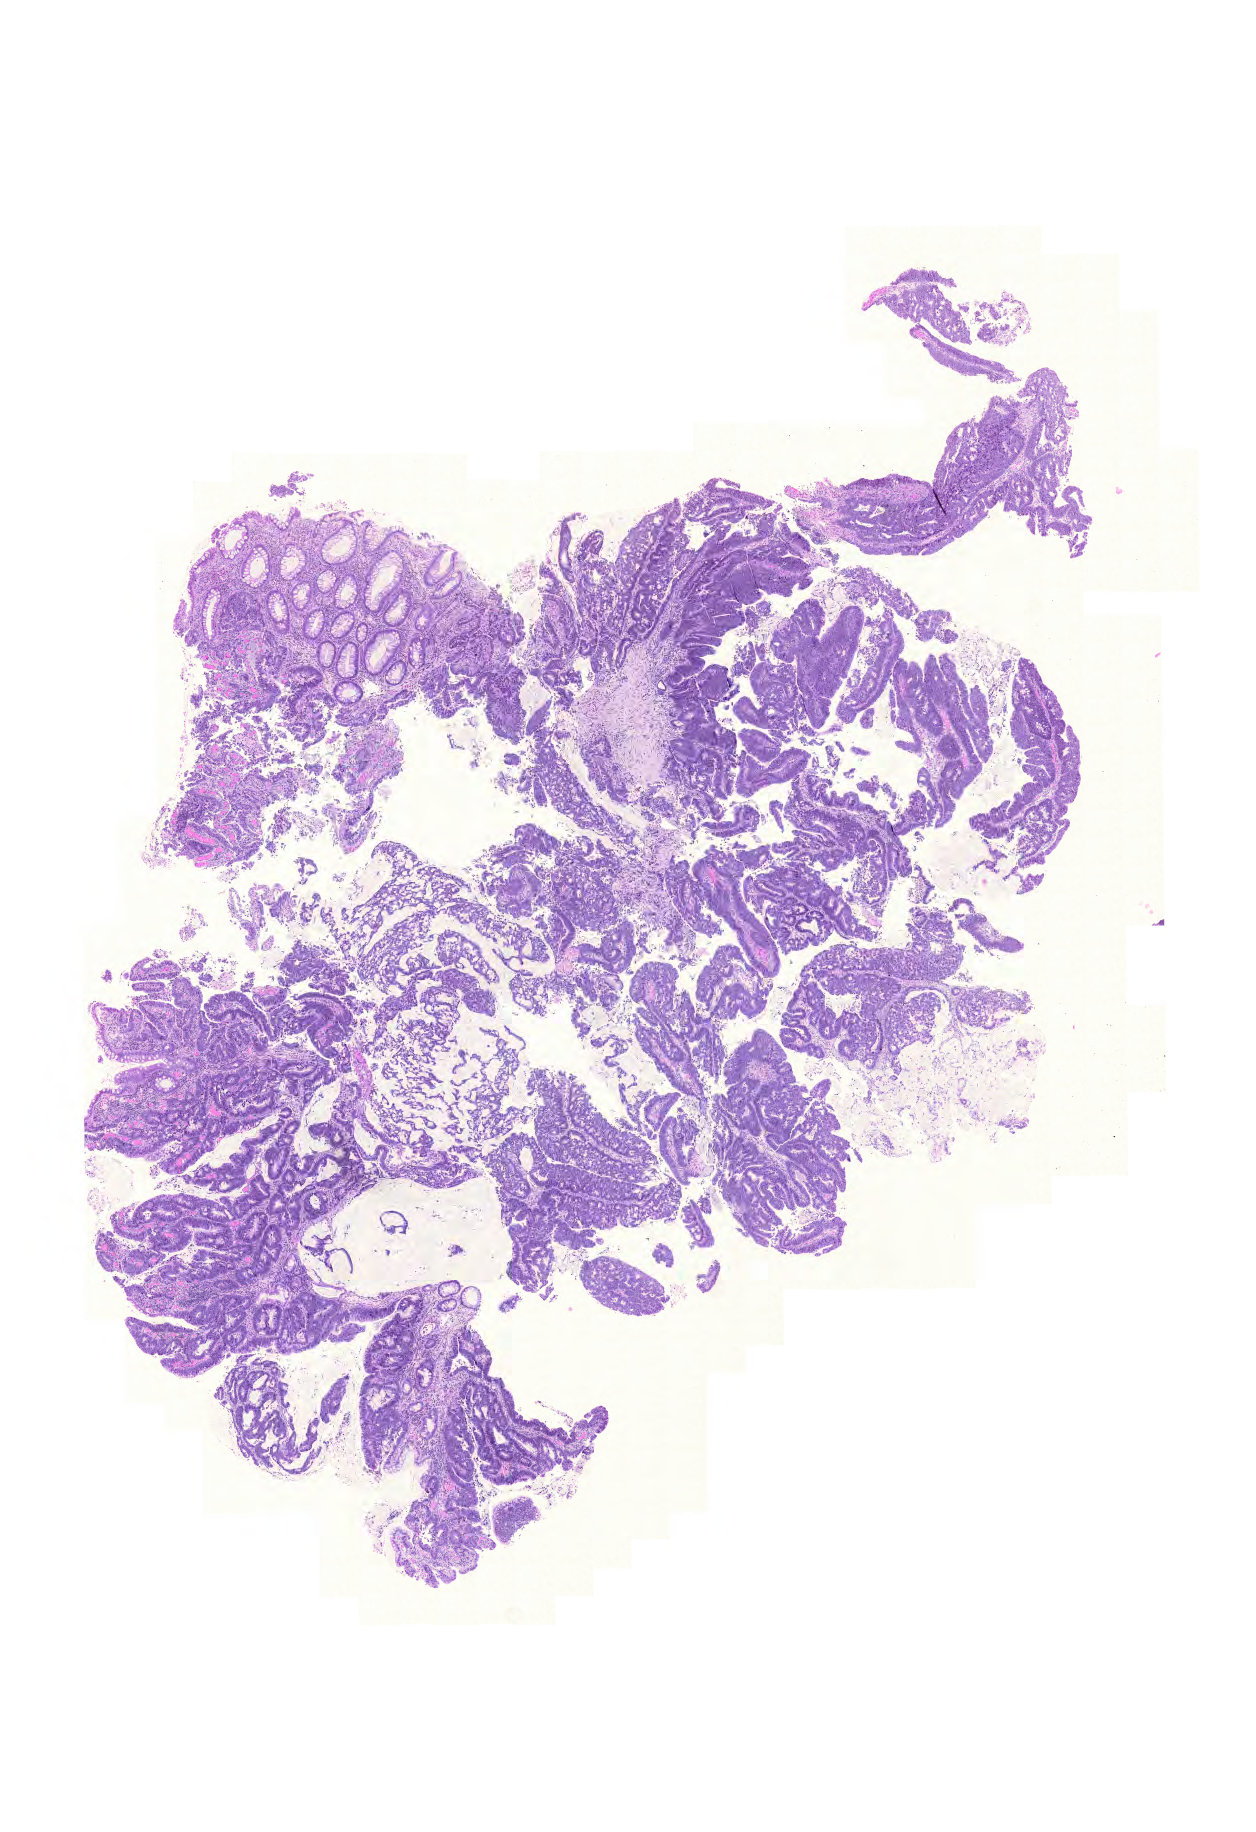
Whole-slide histology image, H&E-stained, a low-resolution overview of the entire scanned area, about 9.3 x 13.6 mm; formalin-fixed paraffin-embedded (FFPE) diagnostic section; primary tumour sample from the colon. Female, age 47 years at initial diagnosis.
* pathologic diagnosis: Mucinous adenocarcinoma
* AJCC pathologic stage: IV (6th edition)
* lymph nodes positive (case pathology): 5 of 30 examined